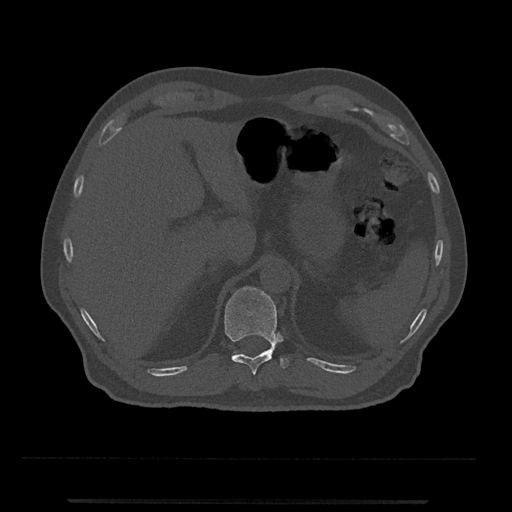
CT including the spine, one axial slice. Slice 458 of 797 in the series (ordered by position). Reconstruction kernel Br40s/3. Bone window (W 1800 / L 400 HU). 0.5 mm slice thickness. 512 × 512 image matrix, field of view 419 × 419 mm. Male patient, age 63 years. Case-level facts recorded for this patient, not image findings: primary cancer: prostate.
Structures marked on this image (semi-automatically segmented with operator editing):
- T11 vertebra: bounding box (x1, y1, x2, y2) in pixels: (224, 286, 288, 375)
- T12 vertebra: (231, 352, 236, 357)